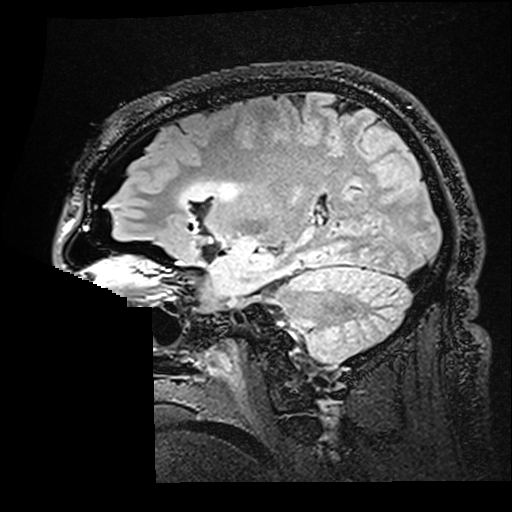
Brain MRI from a brain-tumour surgery series, one sagittal slice; position 114 of 176 along the scan axis; T2 FLAIR; 1 mm slice thickness; 512 × 512 image matrix, field of view 250 × 250 mm. Case-level facts recorded for this patient, not image findings: histopathology: Astrocytoma; WHO grade: 2; IDH mutation: yes.
Outlined on this slice (manually delineated by an expert):
- residual tumour: box from (x=179, y=181) to (x=242, y=208) px